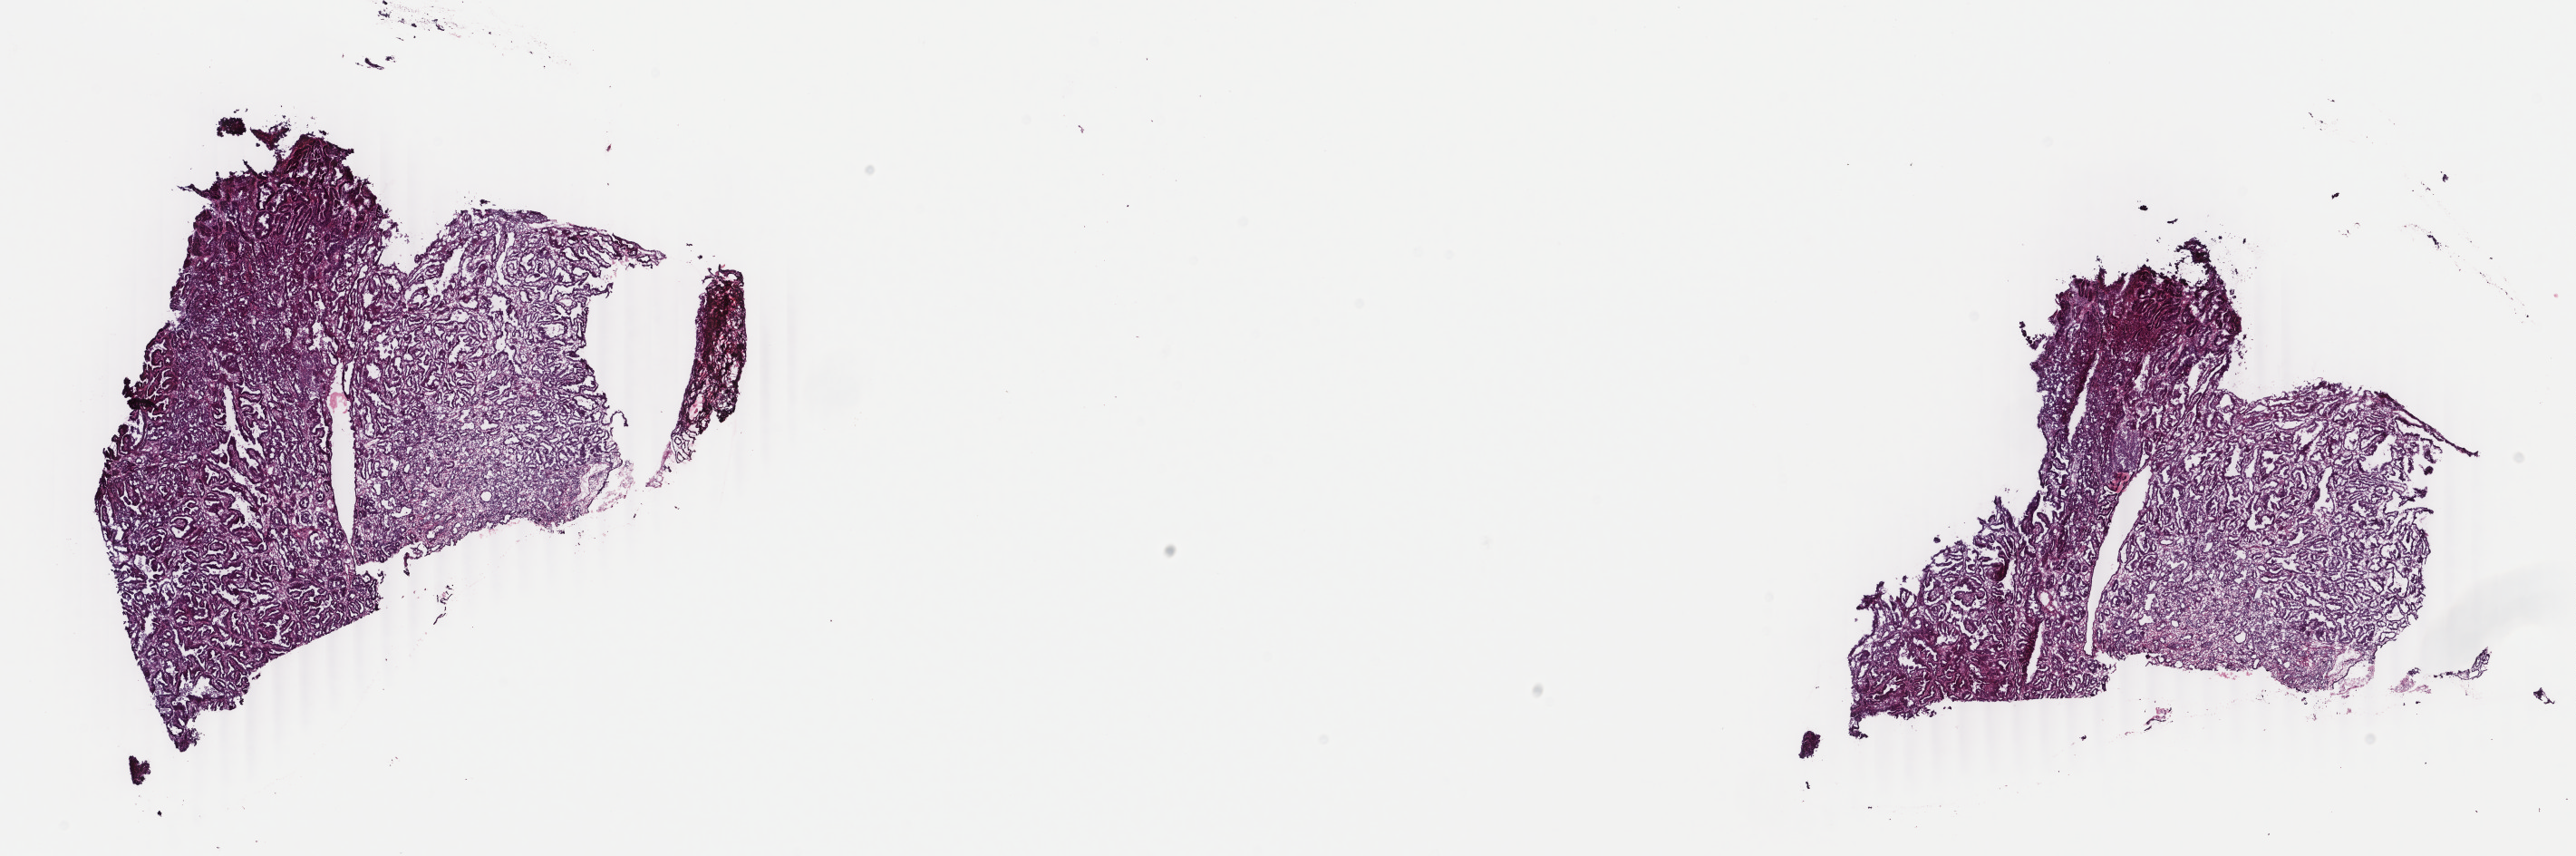
H&E-stained whole-slide image, shown as a low-resolution overview of the whole scanned area (about 22.6 x 7.5 mm, from a 40x scan). Frozen section from the top of the tissue portion. Uterus, primary tumour sample. Patient: female, age at initial diagnosis 72 years. Histologic grade: G3 (poorly differentiated). Composition of this section per pathologist review: tumour cells 90%, tumour nuclei 90%, normal cells 0%, stromal cells 5%, necrosis 5%. Inflammatory infiltration, as recorded: lymphocyte infiltration 40%, monocyte infiltration 20%, neutrophil infiltration 20%.
Lymph nodes positive (case pathology): 0 of 36 examined. FIGO stage: IVB. Diagnosis: Serous cystadenocarcinoma, NOS (endometrium).